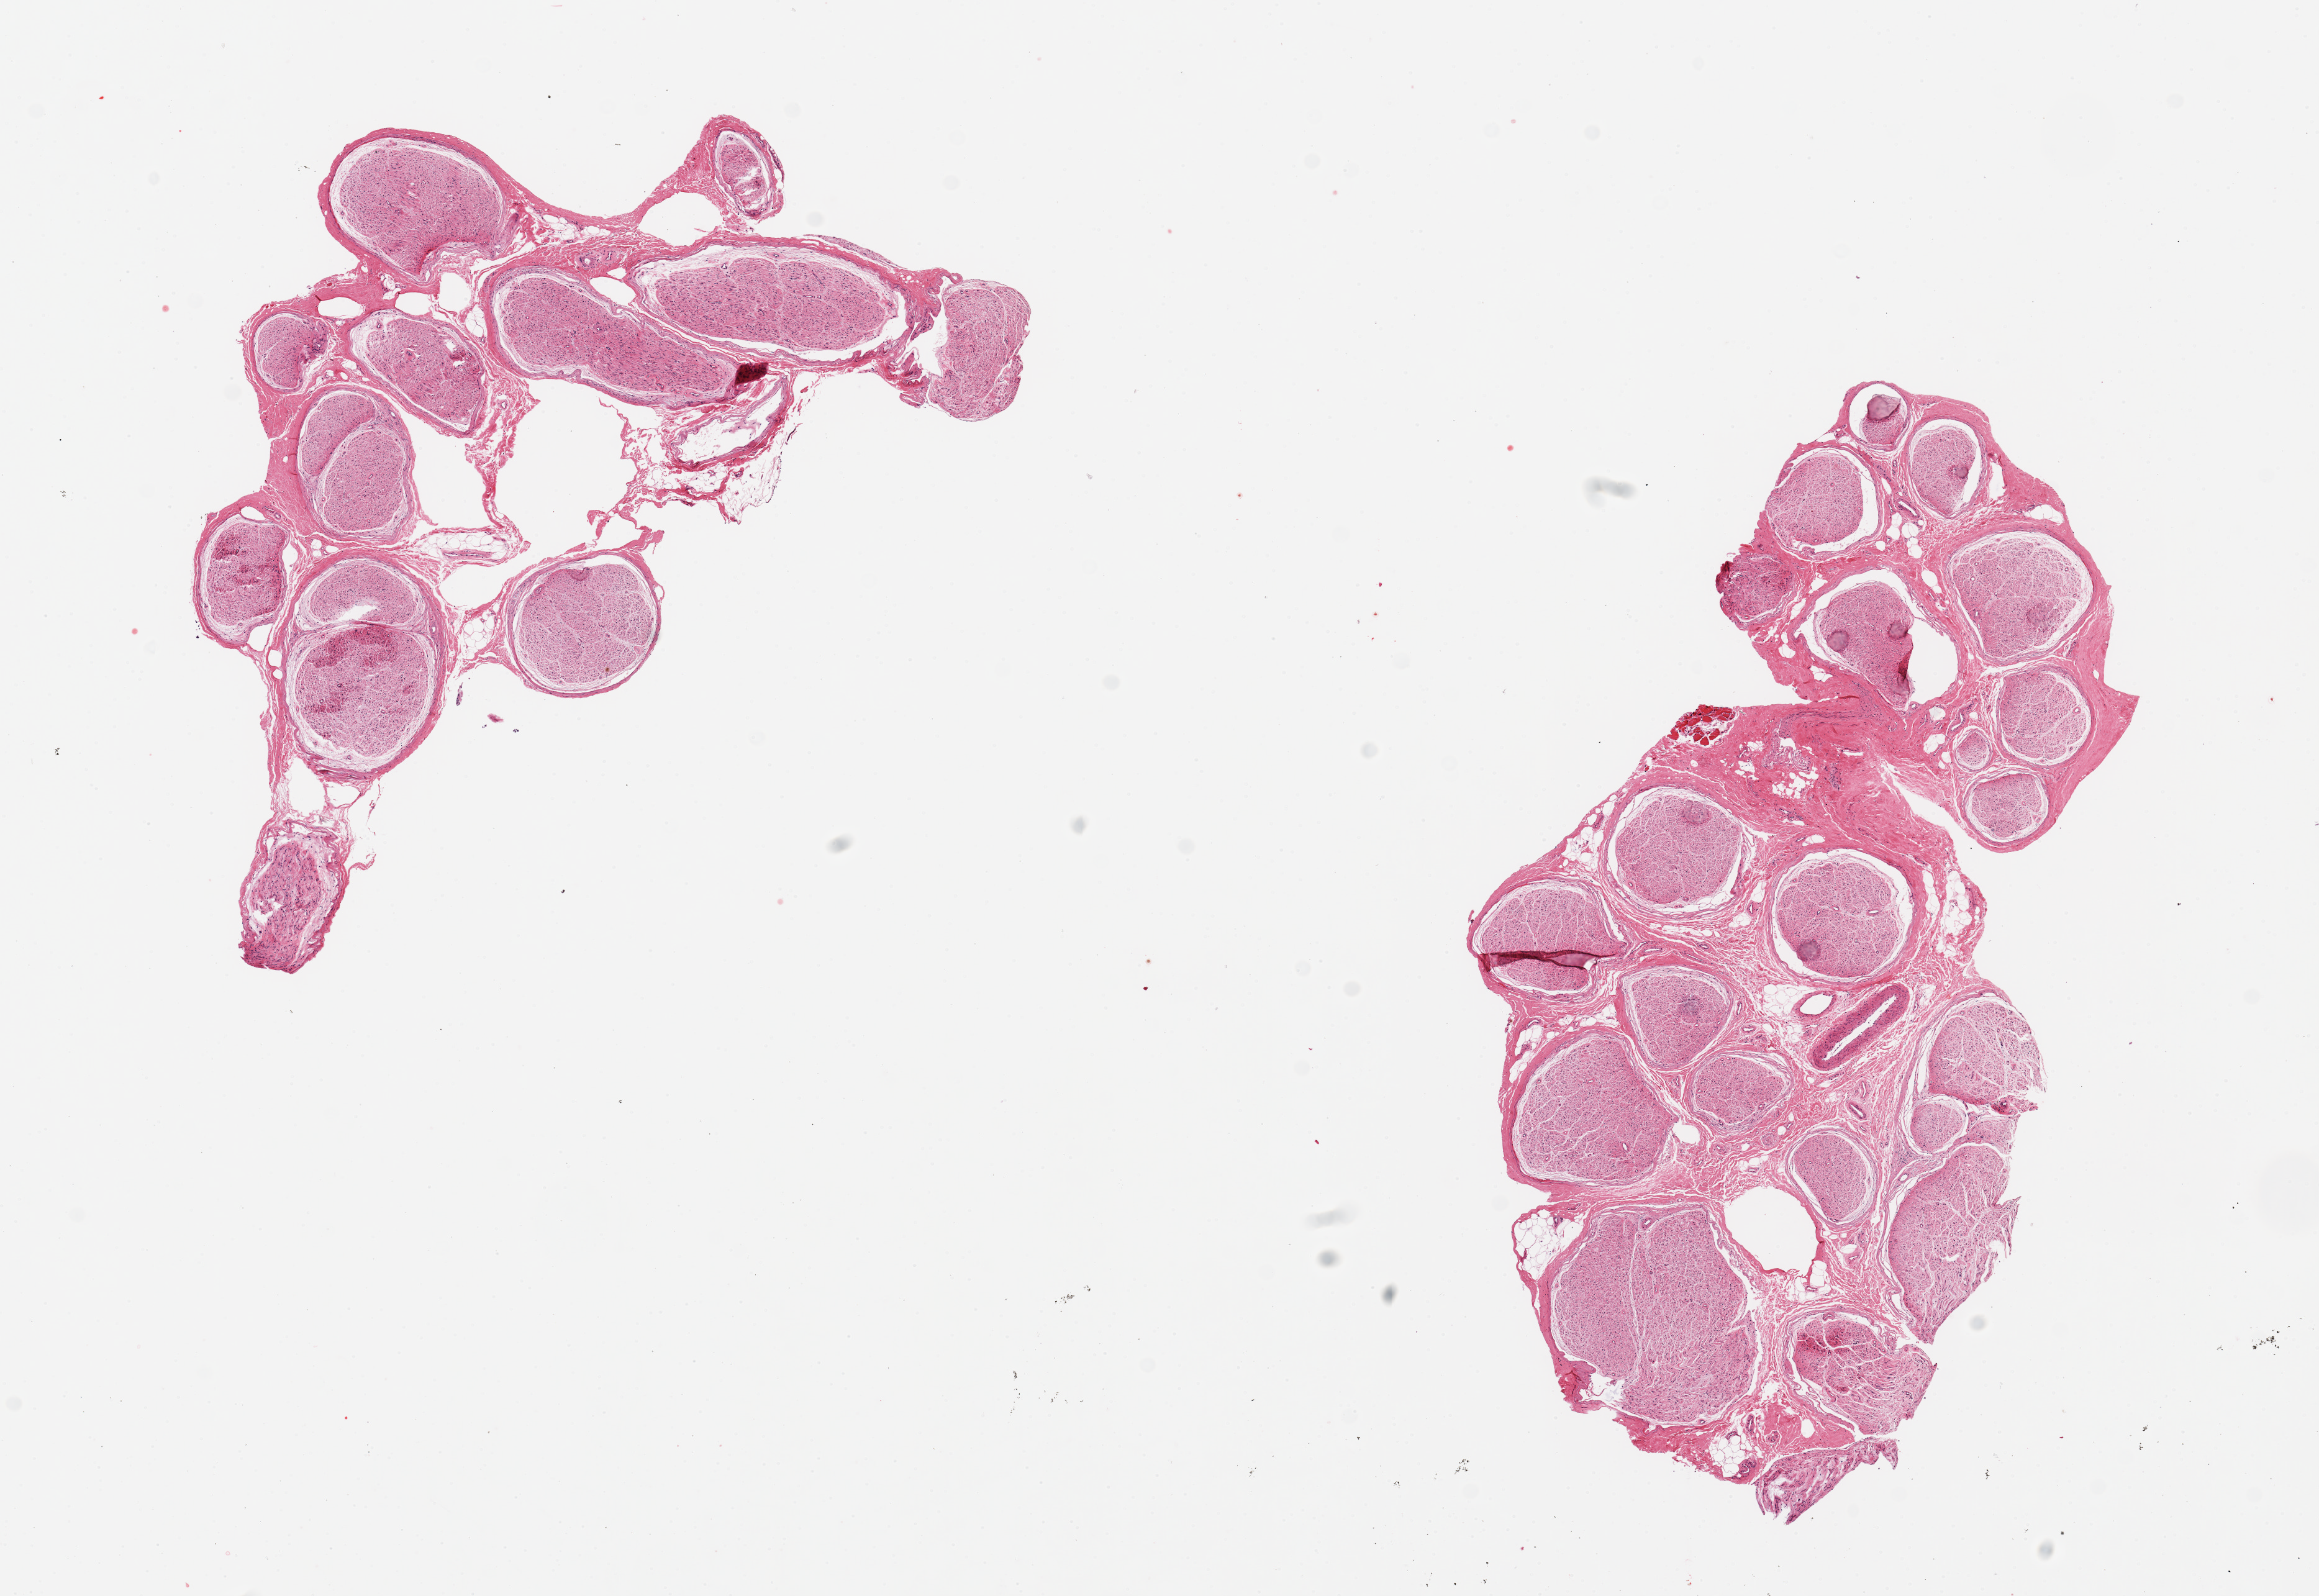
Whole-slide image, hematoxylin and eosin (H&E) stain — a low-resolution overview of the entire scanned area, about 14.8 x 10.2 mm. PAXgene-fixed paraffin-embedded (PFPE) section. Target tissue: tibial nerve. Donor tissue sample. Donor sex: male.
- review note (as recorded): 2 pieces 7x4 & 6x3 mm; minimal adipose